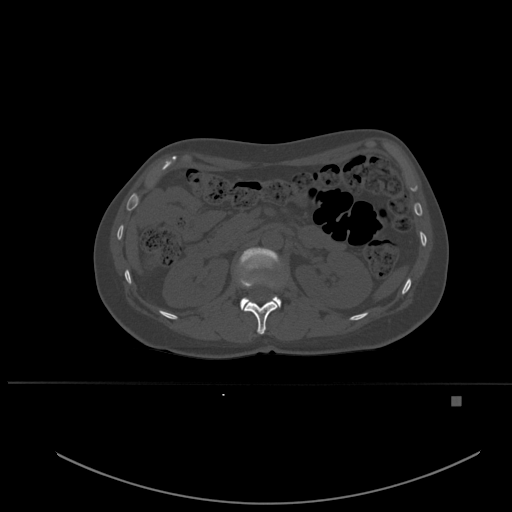
CT including the spine, one axial slice. Slice 245 of 651 in the series (ordered by position). Bone window (W 1800 / L 400 HU). 1.5 mm slice thickness. 512 × 512 image matrix. Patient: female, 49 years. From the clinical record (not read from this slice): primary cancer: breast.
Structures marked on this image (semi-automatically segmented with operator editing):
- L1 vertebra: box from (x=239, y=247) to (x=282, y=310) px
- T12 vertebra: (x=244, y=300)–(x=278, y=335)